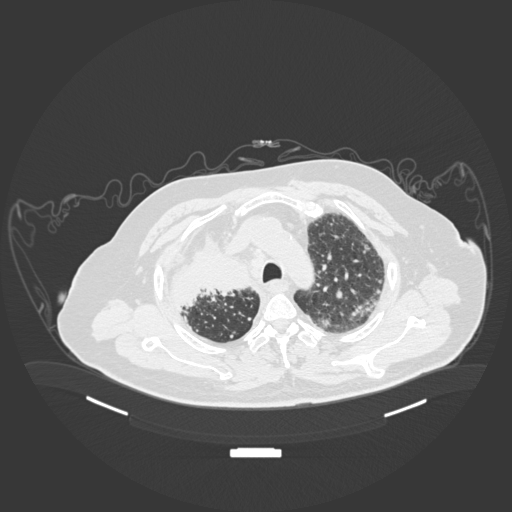
Chest CT, one axial slice; position 148 of 201 along the scan axis; reconstruction kernel B30f; 120 kVp; lung window (W 1500 / L -600 HU); 1 mm slice thickness; 512 × 512 image matrix. Male patient, age 69 years. Case-level facts recorded for this patient, not image findings: clinical TNM (as recorded): T4 N3 M1.
Annotated regions visible in this slice (rectangle marked by the reading radiologist):
- lung tumour (recorded histology: adenocarcinoma): bounding box <165,227,256,313> (left, top, right, bottom; pixels)